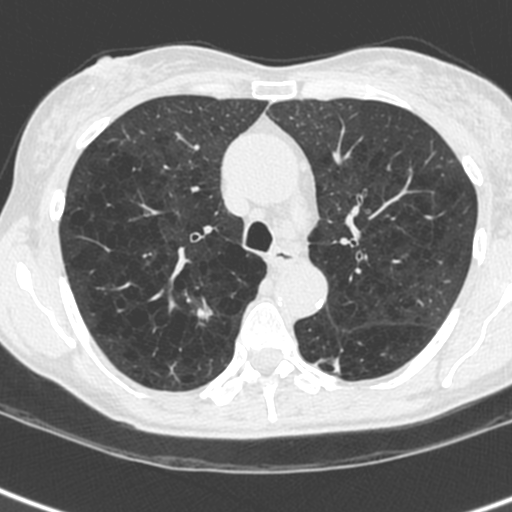
Axial slice from a low-dose chest CT screening exam, baseline annual screen, lung window (W 1500 / L -600 HU), standard (soft-tissue) reconstruction kernel (C), 120 kVp, slice 75 of 238 in the series. Female, age 61 years at enrolment. Current smoker at enrolment.
Expert-annotated lung lesion, bounding box [x1, y1, x2, y2] px = [179, 296, 226, 339]. No non-calcified nodule or mass ≥4 mm was recorded by the screening reader at this exam. Official screen result: negative screen, no significant abnormalities. Later outcome: lung cancer diagnosed 836 days after this screen (after the third annual screen) — non-small cell carcinoma, right upper lobe, undifferentiated (G4), stage IA (AJCC 6th edition), 15 mm at pathology.